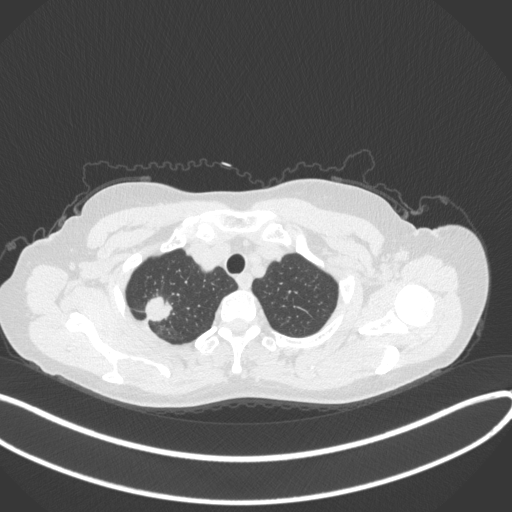
Chest CT, one axial slice; position 318 of 342 along the scan axis; reconstruction kernel B31f; 120 kVp; lung window (W 1500 / L -600 HU); 1 mm slice thickness; 512 × 512 image matrix, field of view 400 × 400 mm. Female patient, age 50 years. From the clinical record (not read from this slice): clinical TNM (as recorded): T1c N0 M0; histopathological grade: G2-3.
Outlined on this slice (bounding box drawn by a radiologist):
- lung tumour (recorded histology: adenocarcinoma): bounding box [x1, y1, x2, y2] px = [144, 294, 174, 325]